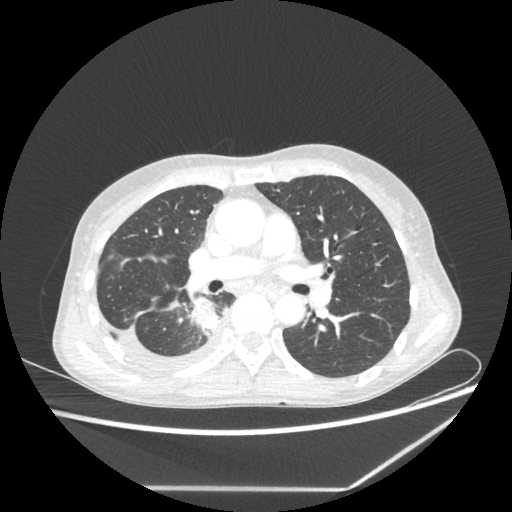
Chest CT, one axial slice. Slice 130 of 237 in the series (ordered by position). Reconstruction kernel STANDARD. Lung window (W 1500 / L -600 HU). 512 × 512 image matrix, field of view 364 × 364 mm. Female patient, age 59 years. Case-level facts recorded for this patient, not image findings: clinical TNM (as recorded): T1c N1 M1.
Annotated regions visible in this slice (bounding box drawn by a radiologist):
- lung tumour (recorded histology: adenocarcinoma): bounding box <188,295,219,336> (left, top, right, bottom; pixels)